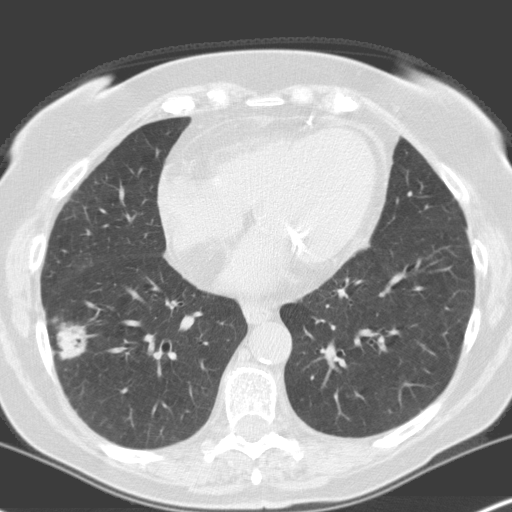
Low-dose screening chest CT, axial slice, baseline annual screen, lung window (W 1500 / L -600 HU), 3.2 mm slice thickness, 512 × 512 image matrix, field of view 316 × 316 mm. Female participant, aged 70 years at enrolment. Current smoker at enrolment.
Expert reader's lesion annotation, bounding box <34,308,100,377> (left, top, right, bottom; pixels). The screening reader recorded 4 non-calcified nodules or masses ≥4 mm on this exam; which of them this box marks is not recorded. Official screen result: positive, change unspecified: nodule(s) >= 4 mm or enlarging nodule(s), mass(es), or other non-specific abnormalities suspicious for lung cancer.